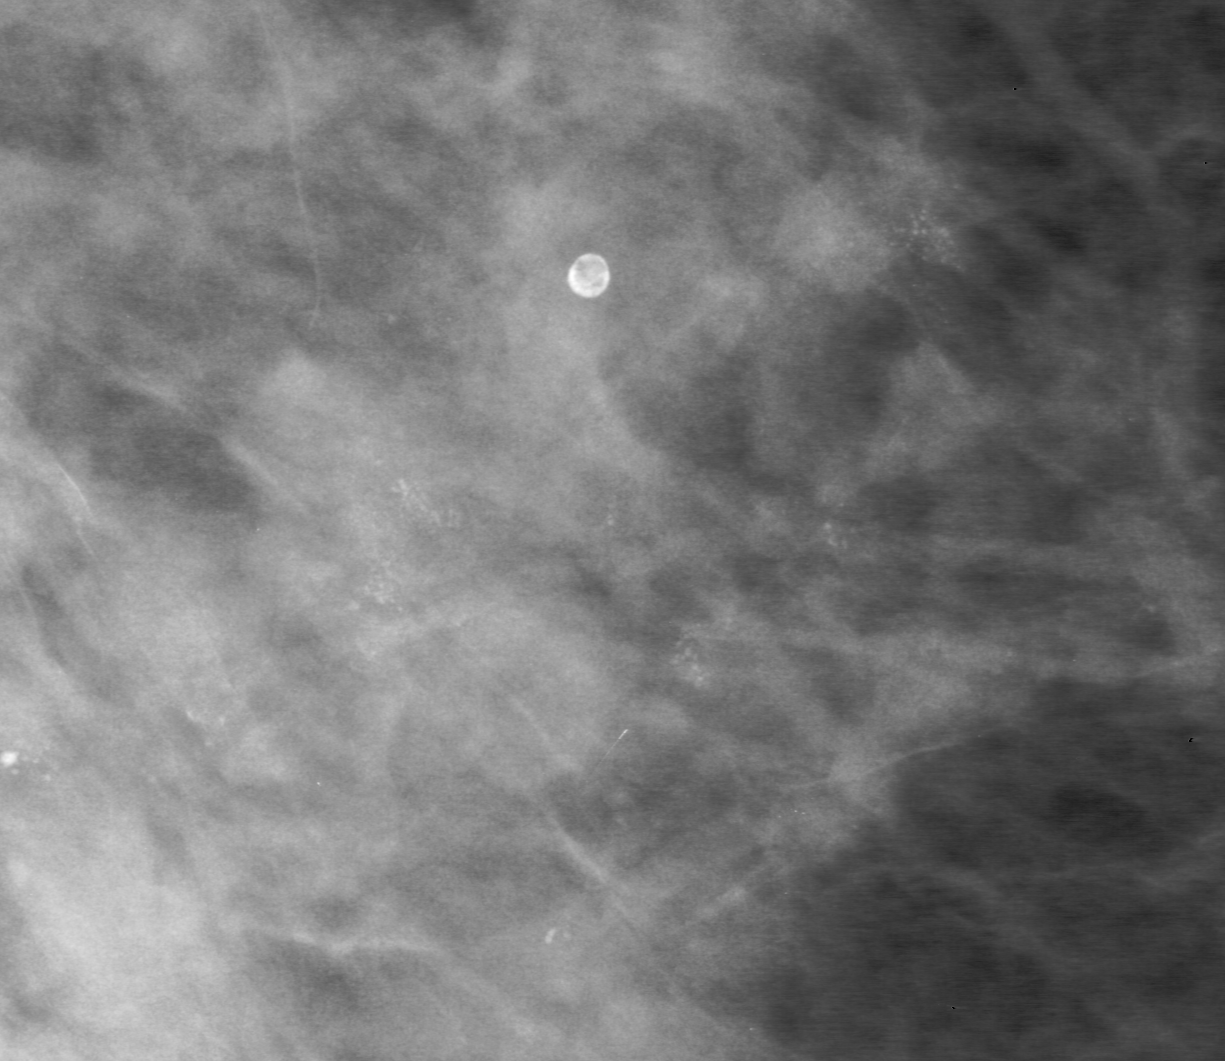
Cropped region of a digitized screen-film mammogram centred on a radiologist-marked abnormality; right breast; CC view; BI-RADS breast density category 3 (scale 1–4).
Finding: calcifications, morphology amorphous, distribution segmental; BI-RADS assessment category 5; pathology (as recorded): malignant.